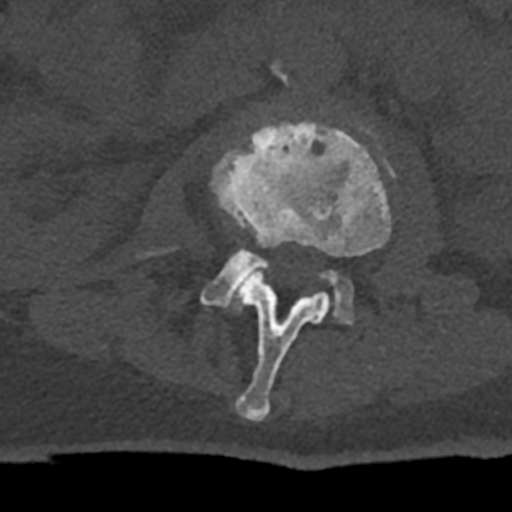
CT including the spine, one axial slice; position 356 of 797 along the scan axis; reconstruction kernel Br40s/3; 120 kVp; bone window (W 1800 / L 400 HU); 0.5 mm slice thickness; 512 × 512 image matrix, field of view 160 × 160 mm. Patient: male, 74 years. Case-level facts recorded for this patient, not image findings: primary cancer: renal; vertebrae with lytic lesions (as recorded): T10, L1, L2, L3, L4, L5.
Structures marked on this image (semi-automatic segmentation, software-assisted and operator-edited):
- L2 vertebra: bounding box <210,120,392,421> (left, top, right, bottom; pixels)
- L3 vertebra: <163,160,388,324>